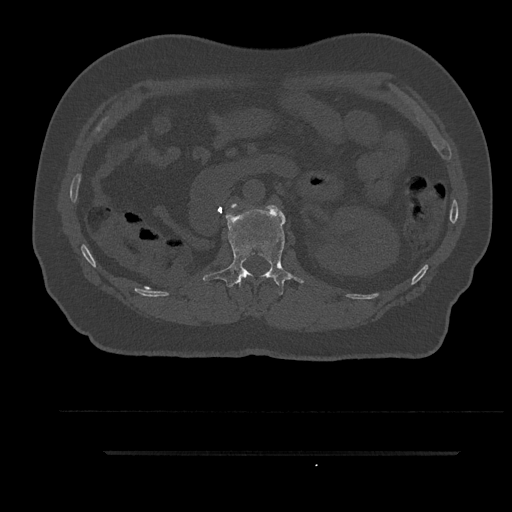
CT including the spine, one axial slice. Position 177 of 797 along the scan axis. Bone window (W 1800 / L 400 HU). 0.5 mm slice thickness. 512 × 512 image matrix, field of view 432 × 432 mm. Male patient, age 63 years. From the clinical record (not read from this slice): primary cancer: renal; vertebrae with lytic lesions (as recorded): T8.
Outlined on this slice (semi-automatic segmentation, software-assisted and operator-edited):
- L1 vertebra: bounding box (x1, y1, x2, y2) in pixels: (203, 205, 304, 295)
- L2 vertebra: (231, 204, 237, 208)
- T12 vertebra: (239, 282, 241, 286)